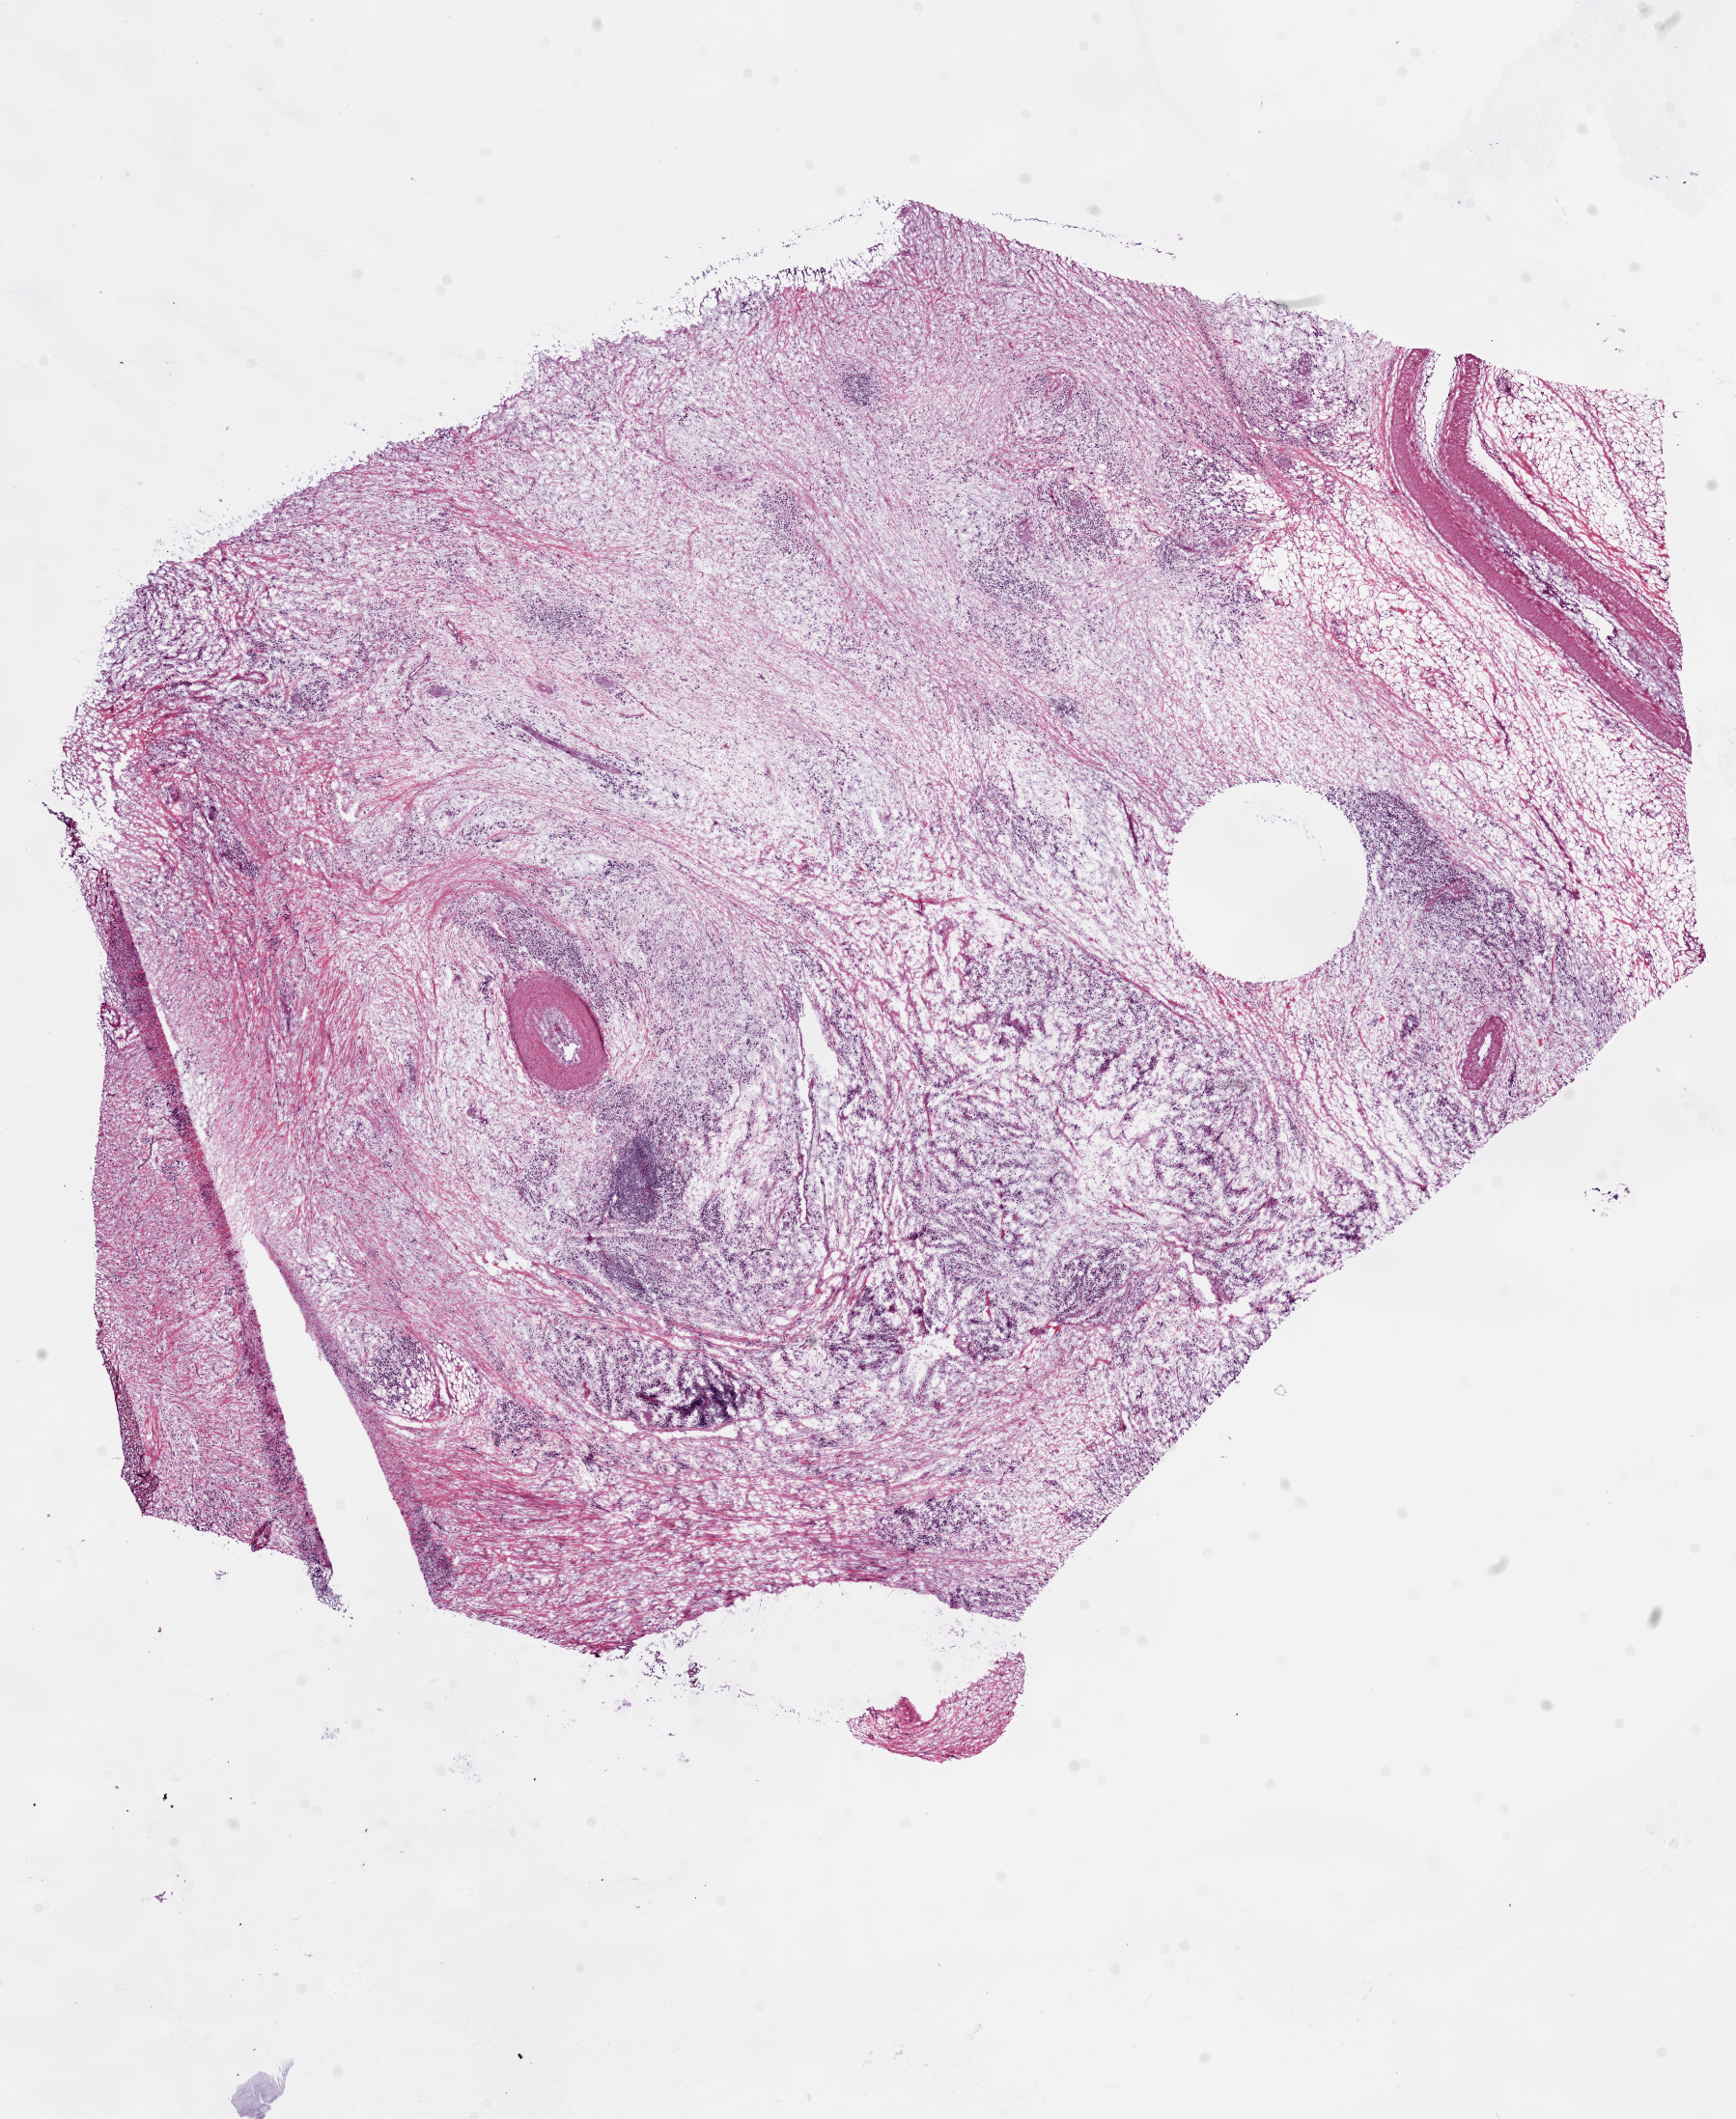
Whole-slide histology image, H&E-stained, low-resolution overview of the scanned area, about 14.5 x 17.7 mm (acquisition: 20x scan); frozen section from the bottom of the tissue portion; primary tumour sample from the stomach. Male, age 60 years at initial diagnosis. Histologic grade: G3 (poorly differentiated). Pathologist review of this section (percent, as recorded): tumour cells 80%, tumour nuclei 75%, normal cells 0%, stromal cells 20%, necrosis 0%.
AJCC pathologic stage: II (6th edition). Diagnosis: Mucinous adenocarcinoma (body of stomach).